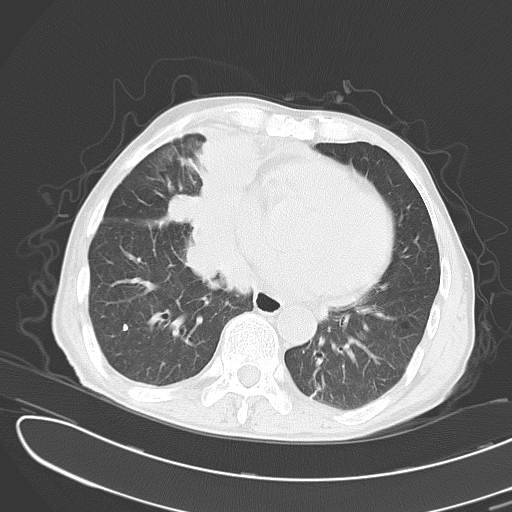
Chest CT, one axial slice. Slice 10 of 43 in the series (ordered by position). 120 kVp. Lung window (W 1500 / L -600 HU). 5 mm slice thickness. 512 × 512 image matrix. Male patient, age 65 years. From the clinical record (not read from this slice): clinical TNM (as recorded): T2 N3 M1; histopathological grade: G3.
Annotated regions visible in this slice (rectangle marked by the reading radiologist):
- lung tumour (recorded histology: small cell carcinoma): bounding box <166,114,250,298> (left, top, right, bottom; pixels)